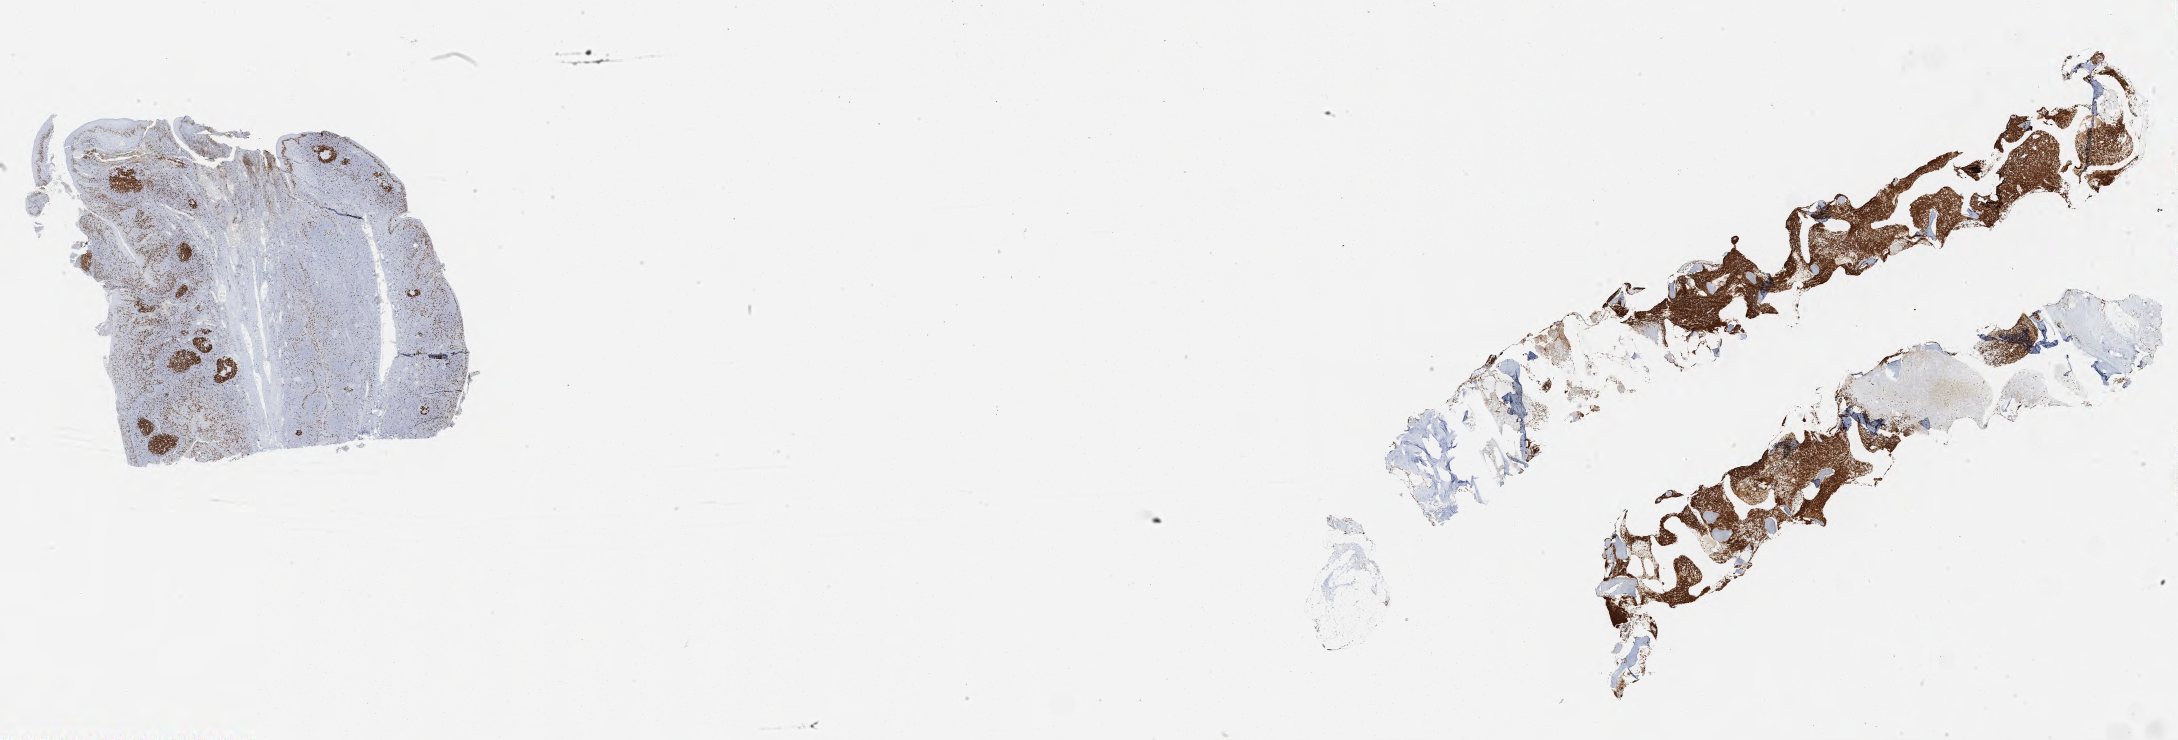
IHC for Ki-67, whole-slide image — low-resolution overview of the scanned area, about 35.0 x 11.9 mm; tumor tissue. Female patient, 60 years old.
* histologic diagnosis: Burkitt lymphoma, NOS